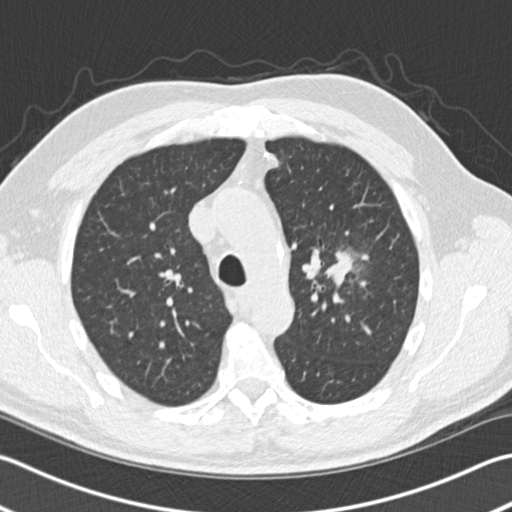
Low-dose screening chest CT, axial slice. Third screening round (two years after baseline). Lung window (W 1500 / L -600 HU). 2 mm slice thickness. Male, age 65 years at enrolment. Former smoker at enrolment.
• Lesion marked by an expert reader, bounding box [x1, y1, x2, y2] px = [306, 240, 370, 304].
• The screening reader recorded 4 non-calcified nodules or masses ≥4 mm on this exam (left upper lobe, left upper lobe, left lower lobe, right middle lobe); which of them this box marks is not recorded.
• Official screen result: positive, other.
• Participant outcome: lung cancer diagnosed 196 days after this screen — acinar cell carcinoma, left upper lobe, stage IA (AJCC 6th edition), 25 mm at pathology.